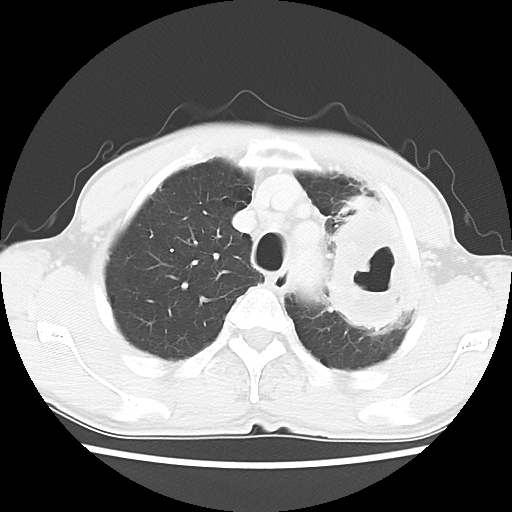
Chest CT, one axial slice. Position 47 of 60 along the scan axis. Reconstruction kernel LUNG. Lung window (W 1500 / L -600 HU). 5 mm slice thickness. 512 × 512 image matrix, field of view 308 × 308 mm. Male patient, age 64 years. Case-level facts recorded for this patient, not image findings: clinical TNM (as recorded): T3 N3 M0.
Outlined on this slice (rectangle marked by the reading radiologist):
- lung tumour (recorded histology: adenocarcinoma): box from (x=312, y=184) to (x=419, y=338) px